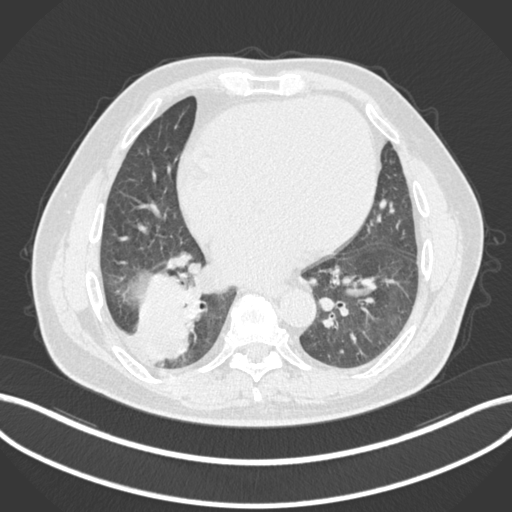
Chest CT, one axial slice. Slice 60 of 200 in the series (ordered by position). 120 kVp. Lung window (W 1500 / L -600 HU). 512 × 512 image matrix. Male patient, age 59 years.
Outlined on this slice (bounding box drawn by a radiologist):
- lung tumour (recorded histology: adenocarcinoma): bounding box <133,274,197,363> (left, top, right, bottom; pixels)